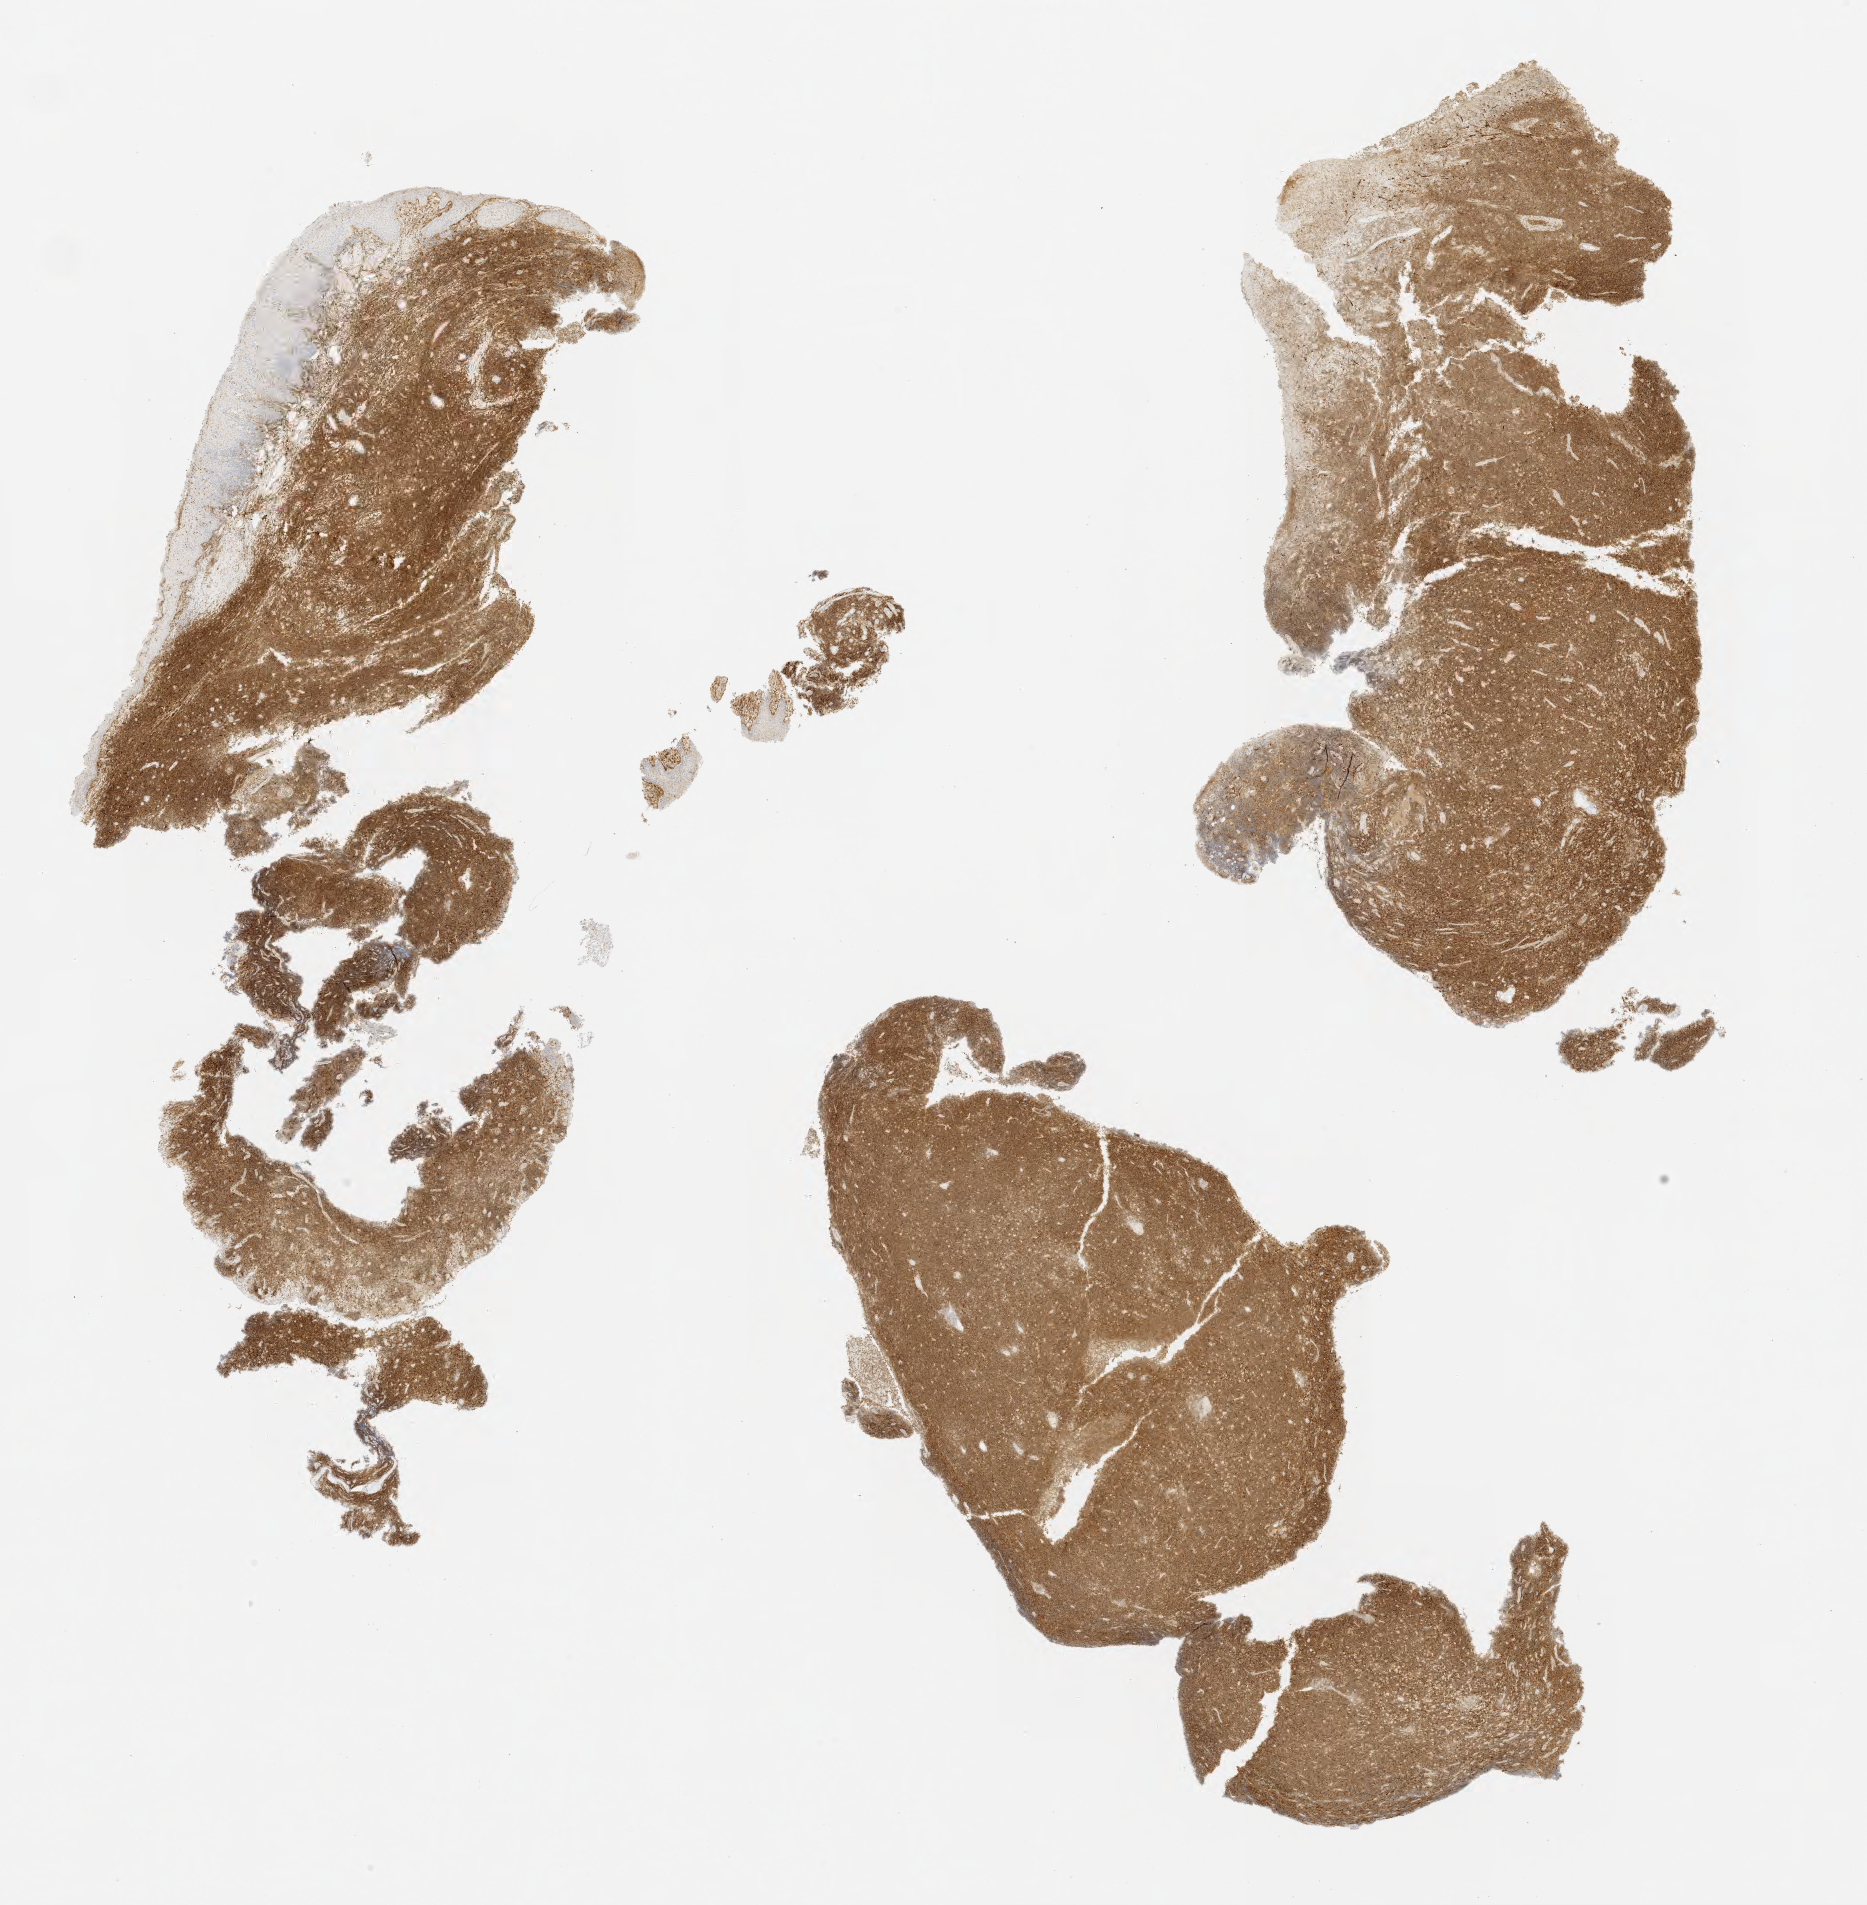
Immunohistochemistry (IHC) whole-slide image stained for CD10, shown as a low-resolution overview of the whole scanned area (about 15.0 x 15.3 mm); tumor tissue. Male patient, aged 22.
- diagnosis: Burkitt lymphoma, NOS